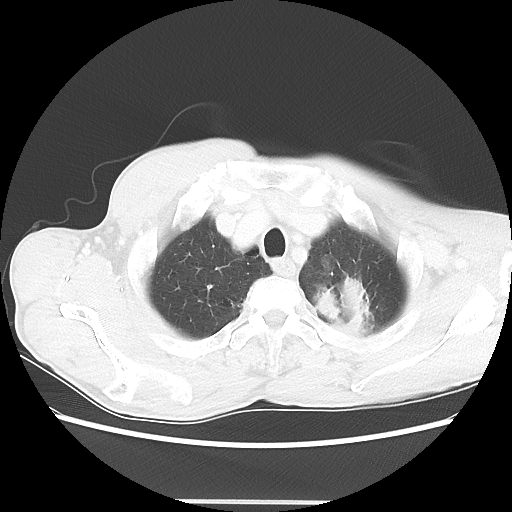
Chest CT, one axial slice. Slice 57 of 62 in the series (ordered by position). Reconstruction kernel LUNG. 100 kVp. Lung window (W 1500 / L -600 HU). 5 mm slice thickness. 512 × 512 image matrix, field of view 360 × 360 mm. Male patient, age 61 years. From the clinical record (not read from this slice): clinical TNM (as recorded): T3 N1 M1.
Annotated regions visible in this slice (bounding box drawn by a radiologist):
- lung tumour (recorded histology: adenocarcinoma): bounding box <307,260,379,336> (left, top, right, bottom; pixels)